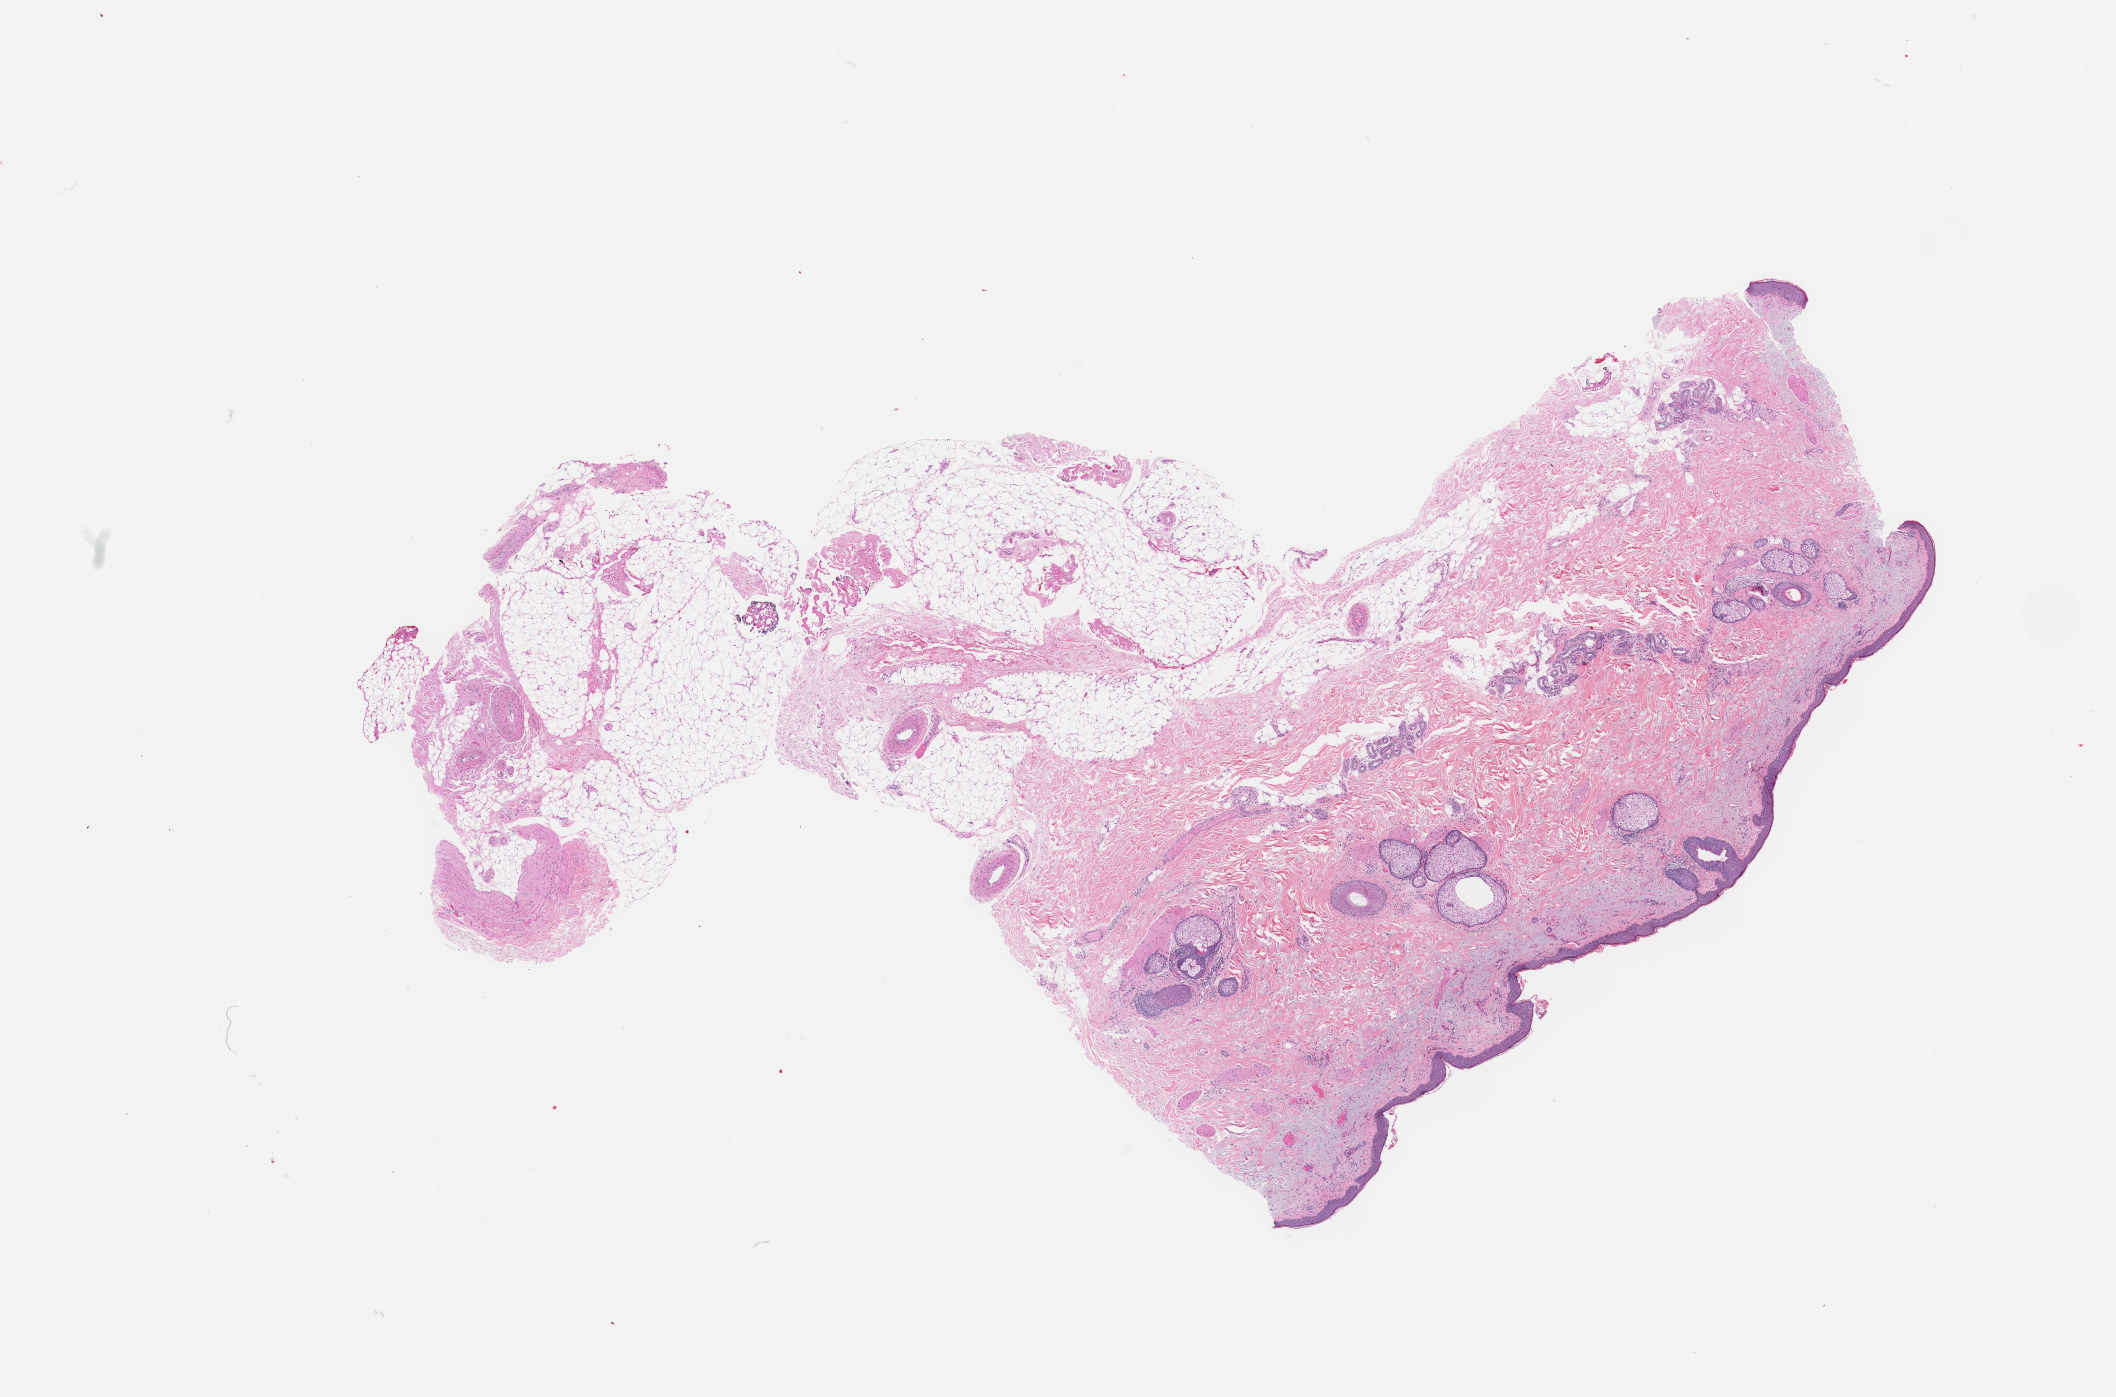
Whole-slide histology image, Hematoxylin and eosin (H&E) stained — low-resolution overview of the scanned area, about 16.7 x 11.0 mm; normal (non-tumour) tissue sample, sampled site: skin. 71-year-old male patient.
This section: normal (non-tumour) tissue from the same patient. Patient diagnosis: Malignant melanoma, NOS.